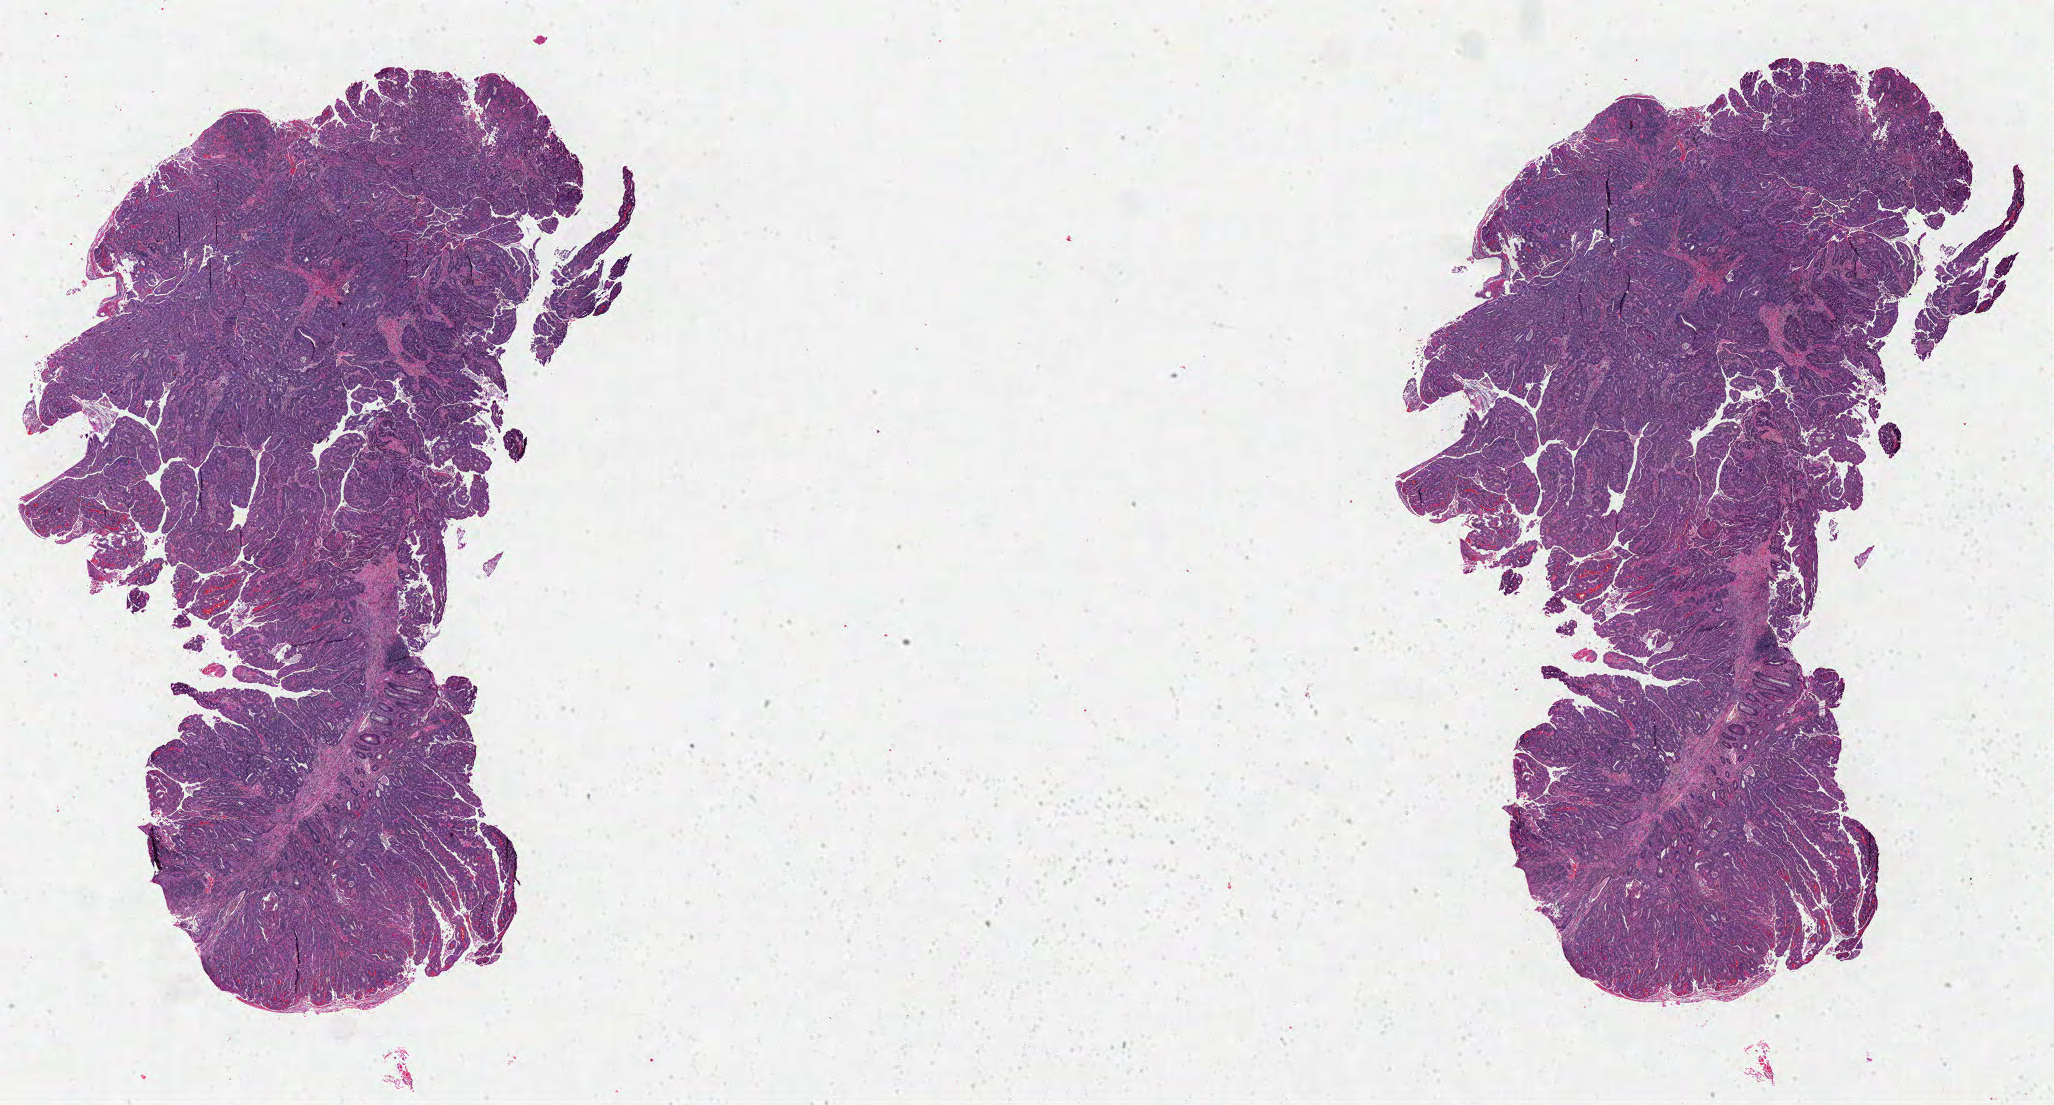
Whole-slide histology image, H&E-stained — shown as a low-resolution overview of the whole scanned area (about 32.3 x 17.4 mm, acquisition: 40x scan), formalin-fixed paraffin-embedded (FFPE) diagnostic section, colon, primary tumour sample. Female, age 65 years at initial diagnosis.
• lymph nodes positive (case pathology): 1 of 24 examined
• histologic diagnosis: Adenocarcinoma, NOS
• TNM: T3 N1a M1
• AJCC pathologic stage: IVA (7th edition)